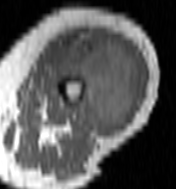
MRI of an extremity soft-tissue mass, one axial slice. Slice 46 of 100 in the series (ordered by position). MR volume resampled by the dataset authors to the PET/CT grid (not the native acquisition matrix). 3.27 mm slice thickness. 176 × 189 image matrix, field of view 172 × 185 mm. Female patient. Case-level facts recorded for this patient, not image findings: histological type: undifferentiated – high grade; grade: high; site of the primary tumour: left thigh.
Annotated regions visible in this slice (expert contour drawn on MRI and transferred to this co-registered scan by the dataset authors):
- gross tumour volume including surrounding oedema: bounding box [x1, y1, x2, y2] px = [55, 32, 141, 136]
- gross tumour volume (mass): [60, 38, 141, 136]